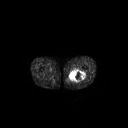
FDG PET of an extremity soft-tissue mass (from a PET/CT study), one axial slice; slice 249 of 267 in the series (ordered by position); 128 × 128 image matrix, field of view 700 × 700 mm. Patient: male, 44 years. From the clinical record (not read from this slice): histological type: undifferentiated pleomorphic liposarcoma; grade: high; site of the primary tumour: left thigh.
Outlined on this slice (expert contour drawn on MRI and transferred to this co-registered scan by the dataset authors):
- gross tumour volume including surrounding oedema: bounding box (x1, y1, x2, y2) in pixels: (68, 69, 86, 83)
- gross tumour volume (mass): (69, 69, 86, 81)